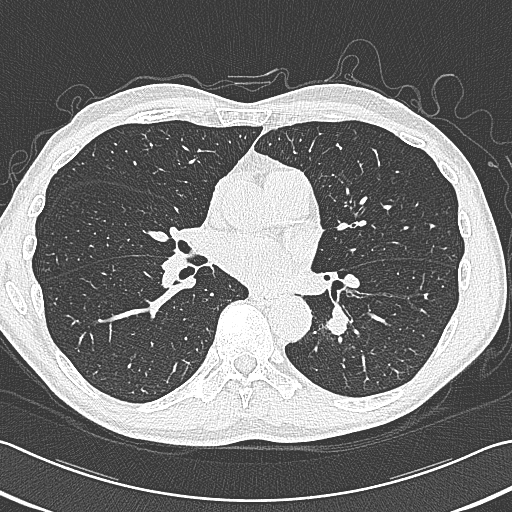
Axial slice from a low-dose chest CT screening exam; baseline screening round; lung window (W 1500 / L -600 HU); 1 mm slice thickness; slice 181 of 354 in the series; 512 × 512 image matrix. Male, age 59 years at enrolment. Former smoker at enrolment.
Expert reader's lesion annotation, box from (x=312, y=296) to (x=376, y=353) px. Screening reader's record for this exam (one nodule recorded; not confirmed to be the boxed lesion): non-calcified nodule or mass ≥4 mm, left lower lobe, 15 × 15 mm, smooth margins, soft tissue attenuation. Later outcome: lung cancer diagnosed 17 days after this screen — squamous cell carcinoma, large cell, nonkeratinizing, NOS, left lower lobe, poorly differentiated (G3), stage IB (AJCC 6th edition), 31 mm at pathology.